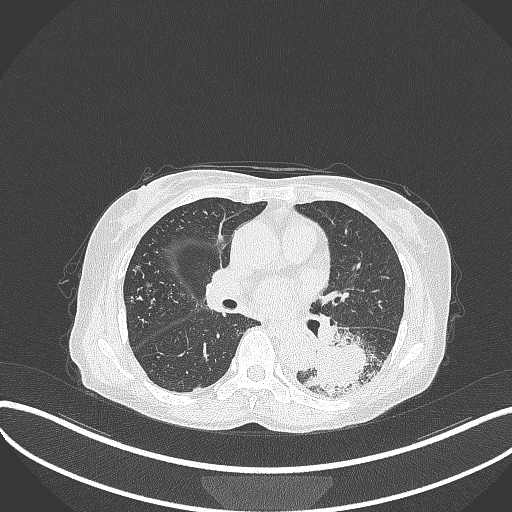
Chest CT, one axial slice; position 166 of 370 along the scan axis; lung window (W 1500 / L -600 HU); 1 mm slice thickness; 512 × 512 image matrix. Female patient, age 78 years. Case-level facts recorded for this patient, not image findings: clinical TNM (as recorded): T3 N0 M1.
Annotated regions visible in this slice (bounding box drawn by a radiologist):
- lung tumour (recorded histology: squamous cell carcinoma): bounding box (x1, y1, x2, y2) in pixels: (298, 337, 380, 396)